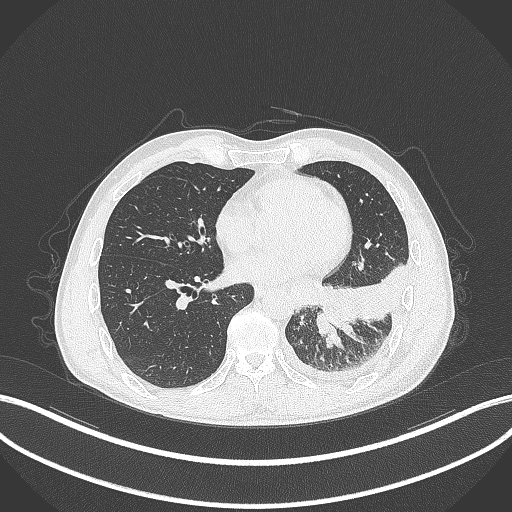
Chest CT, one axial slice. Position 120 of 295 along the scan axis. Reconstruction kernel B70f. Lung window (W 1500 / L -600 HU). 1 mm slice thickness. 512 × 512 image matrix. Patient: male, 47 years. Case-level facts recorded for this patient, not image findings: clinical TNM (as recorded): T3 N1 M1c; histopathological grade: G3.
Annotated regions visible in this slice (rectangle marked by the reading radiologist):
- lung tumour (recorded histology: small cell carcinoma): bounding box <313,296,362,339> (left, top, right, bottom; pixels)